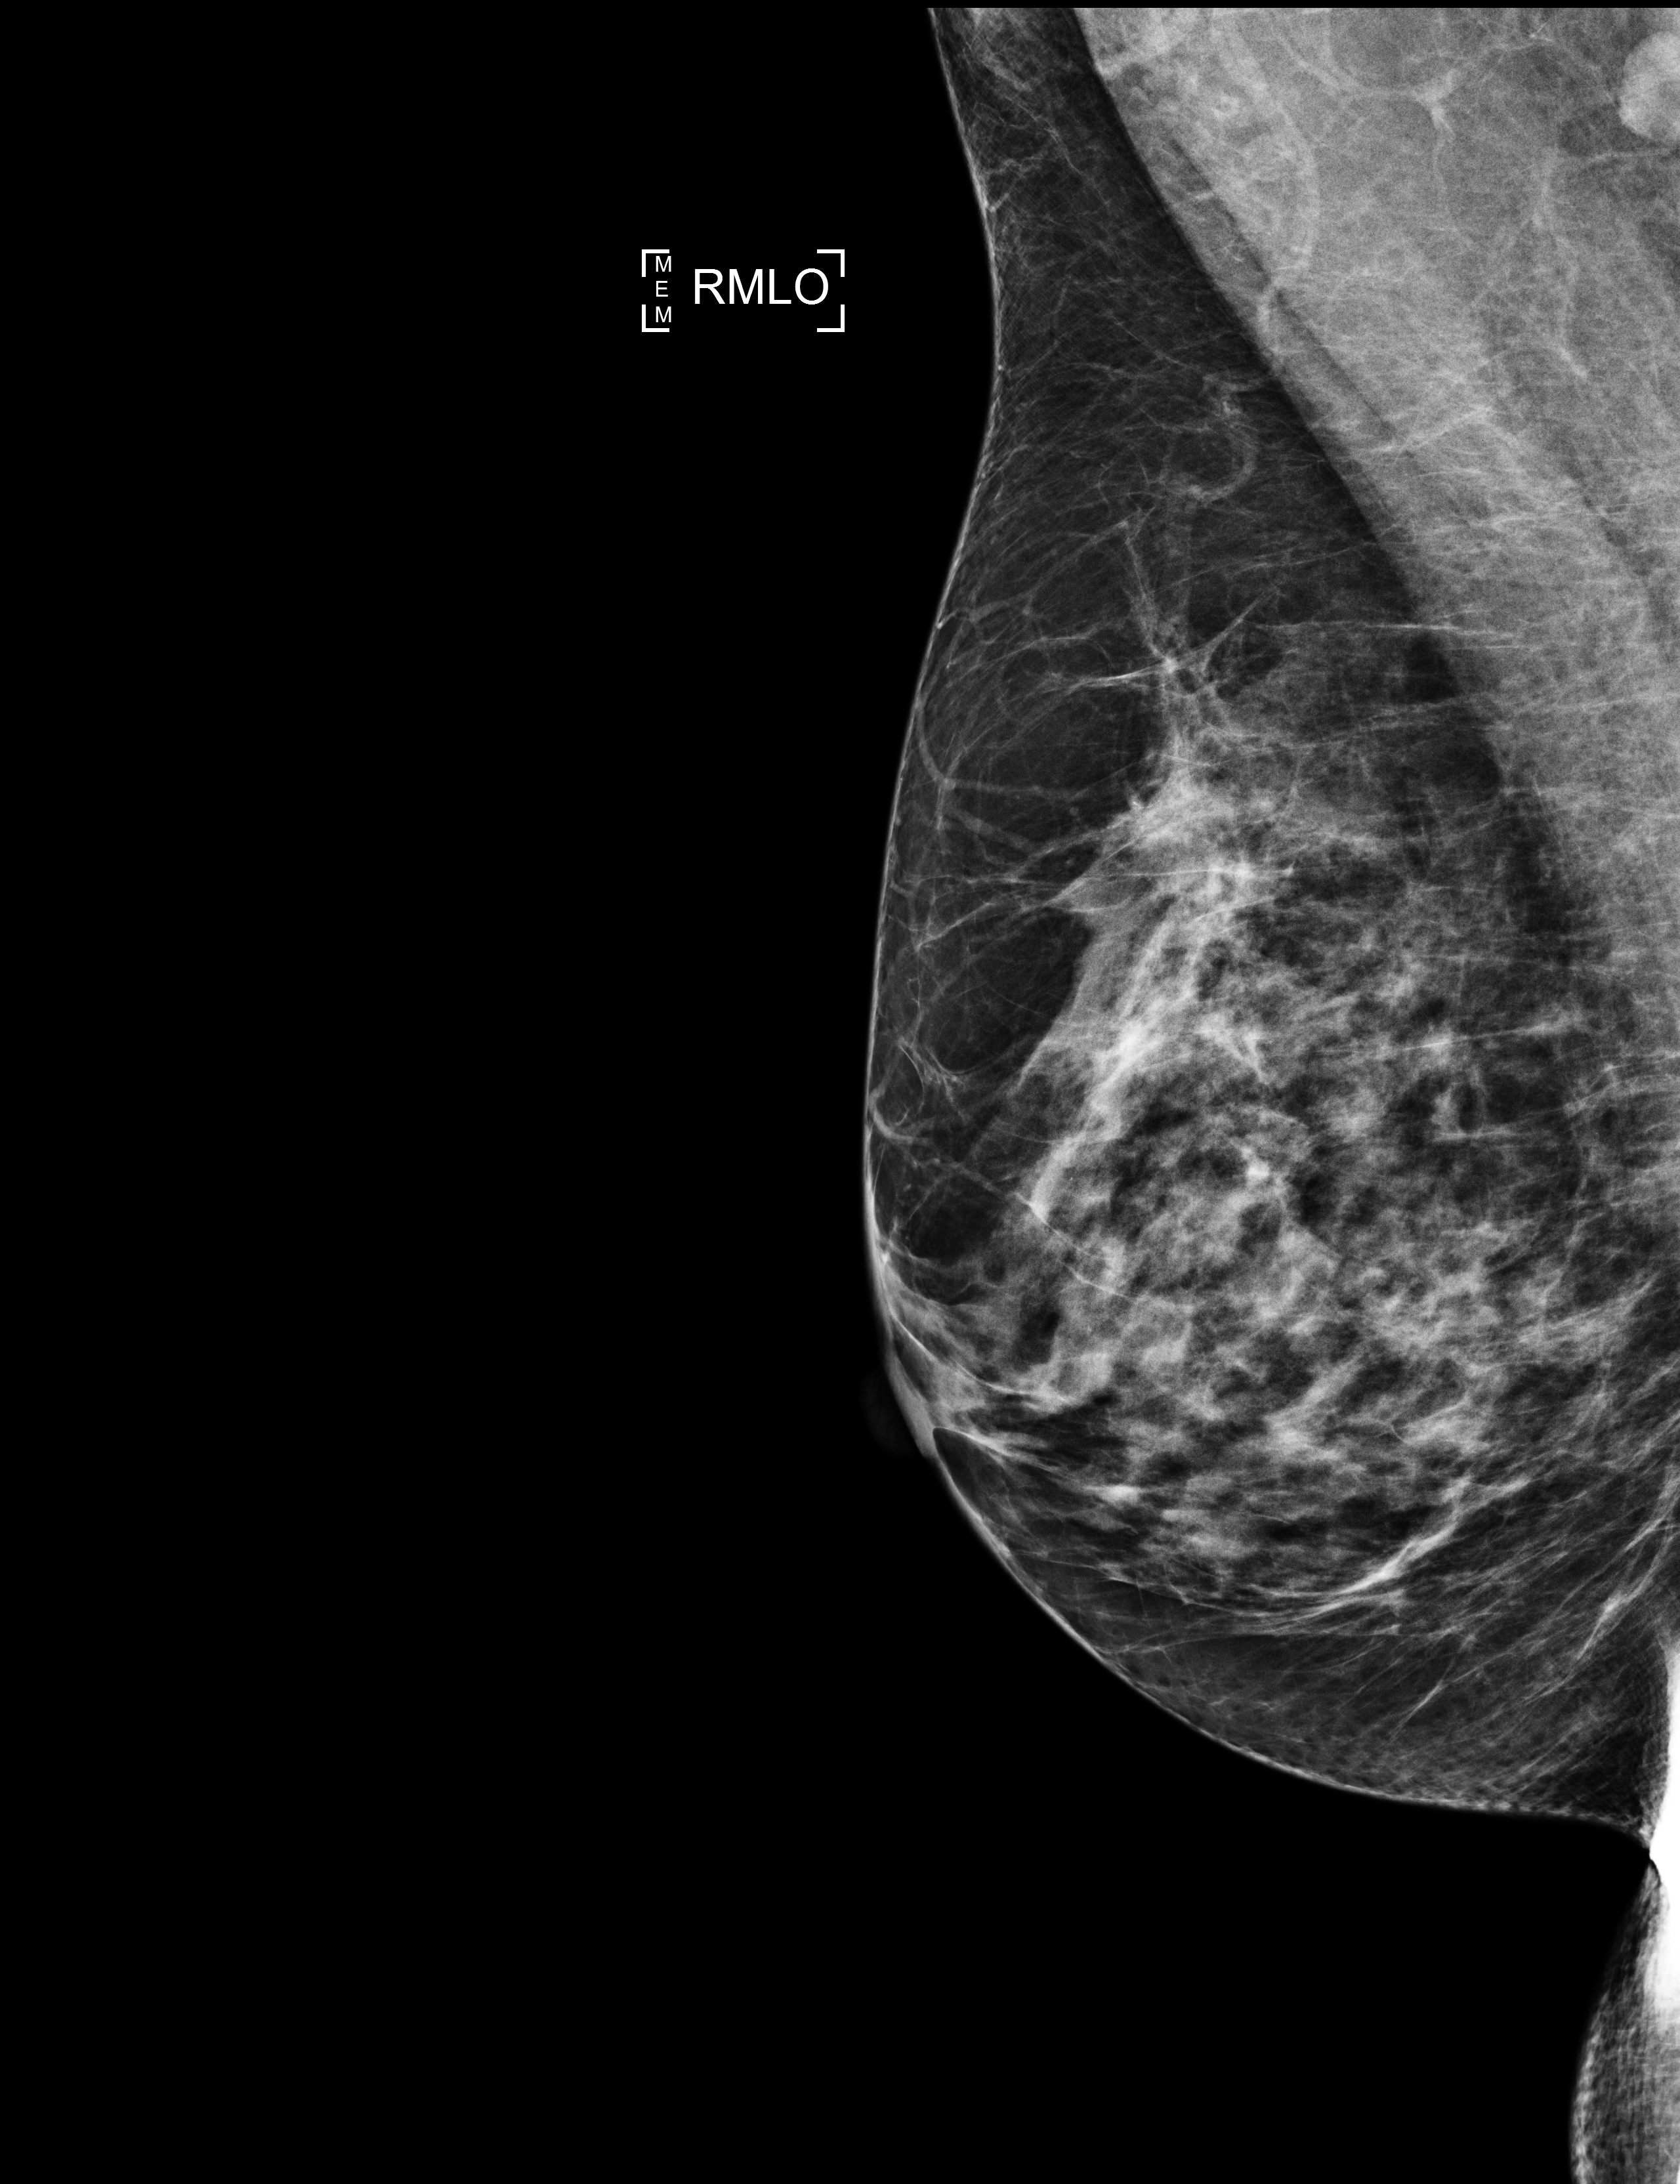
Full-field digital mammogram (FFDM); right breast; mediolateral oblique (MLO) view; screening examination. Female patient, age 57 years.
- BI-RADS breast density category at the screening exam (both breasts, scale 1–4): 3
- final BI-RADS assessment for this screening round (tomosynthesis exam, both breasts): category 1
- recall: no recall after this screen